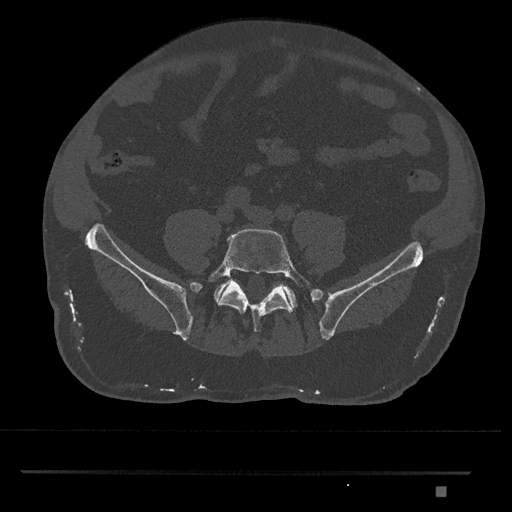
CT including the spine, one axial slice. Slice 550 of 1134 in the series (ordered by position). Reconstruction kernel Br40s/3. 120 kVp. Bone window (W 1800 / L 400 HU). 0.5 mm slice thickness. 512 × 512 image matrix. Male patient, age 65 years. Case-level facts recorded for this patient, not image findings: primary cancer: prostate.
Outlined on this slice (semi-automatic segmentation, software-assisted and operator-edited):
- L5 vertebra: bounding box (x1, y1, x2, y2) in pixels: (208, 228, 311, 333)